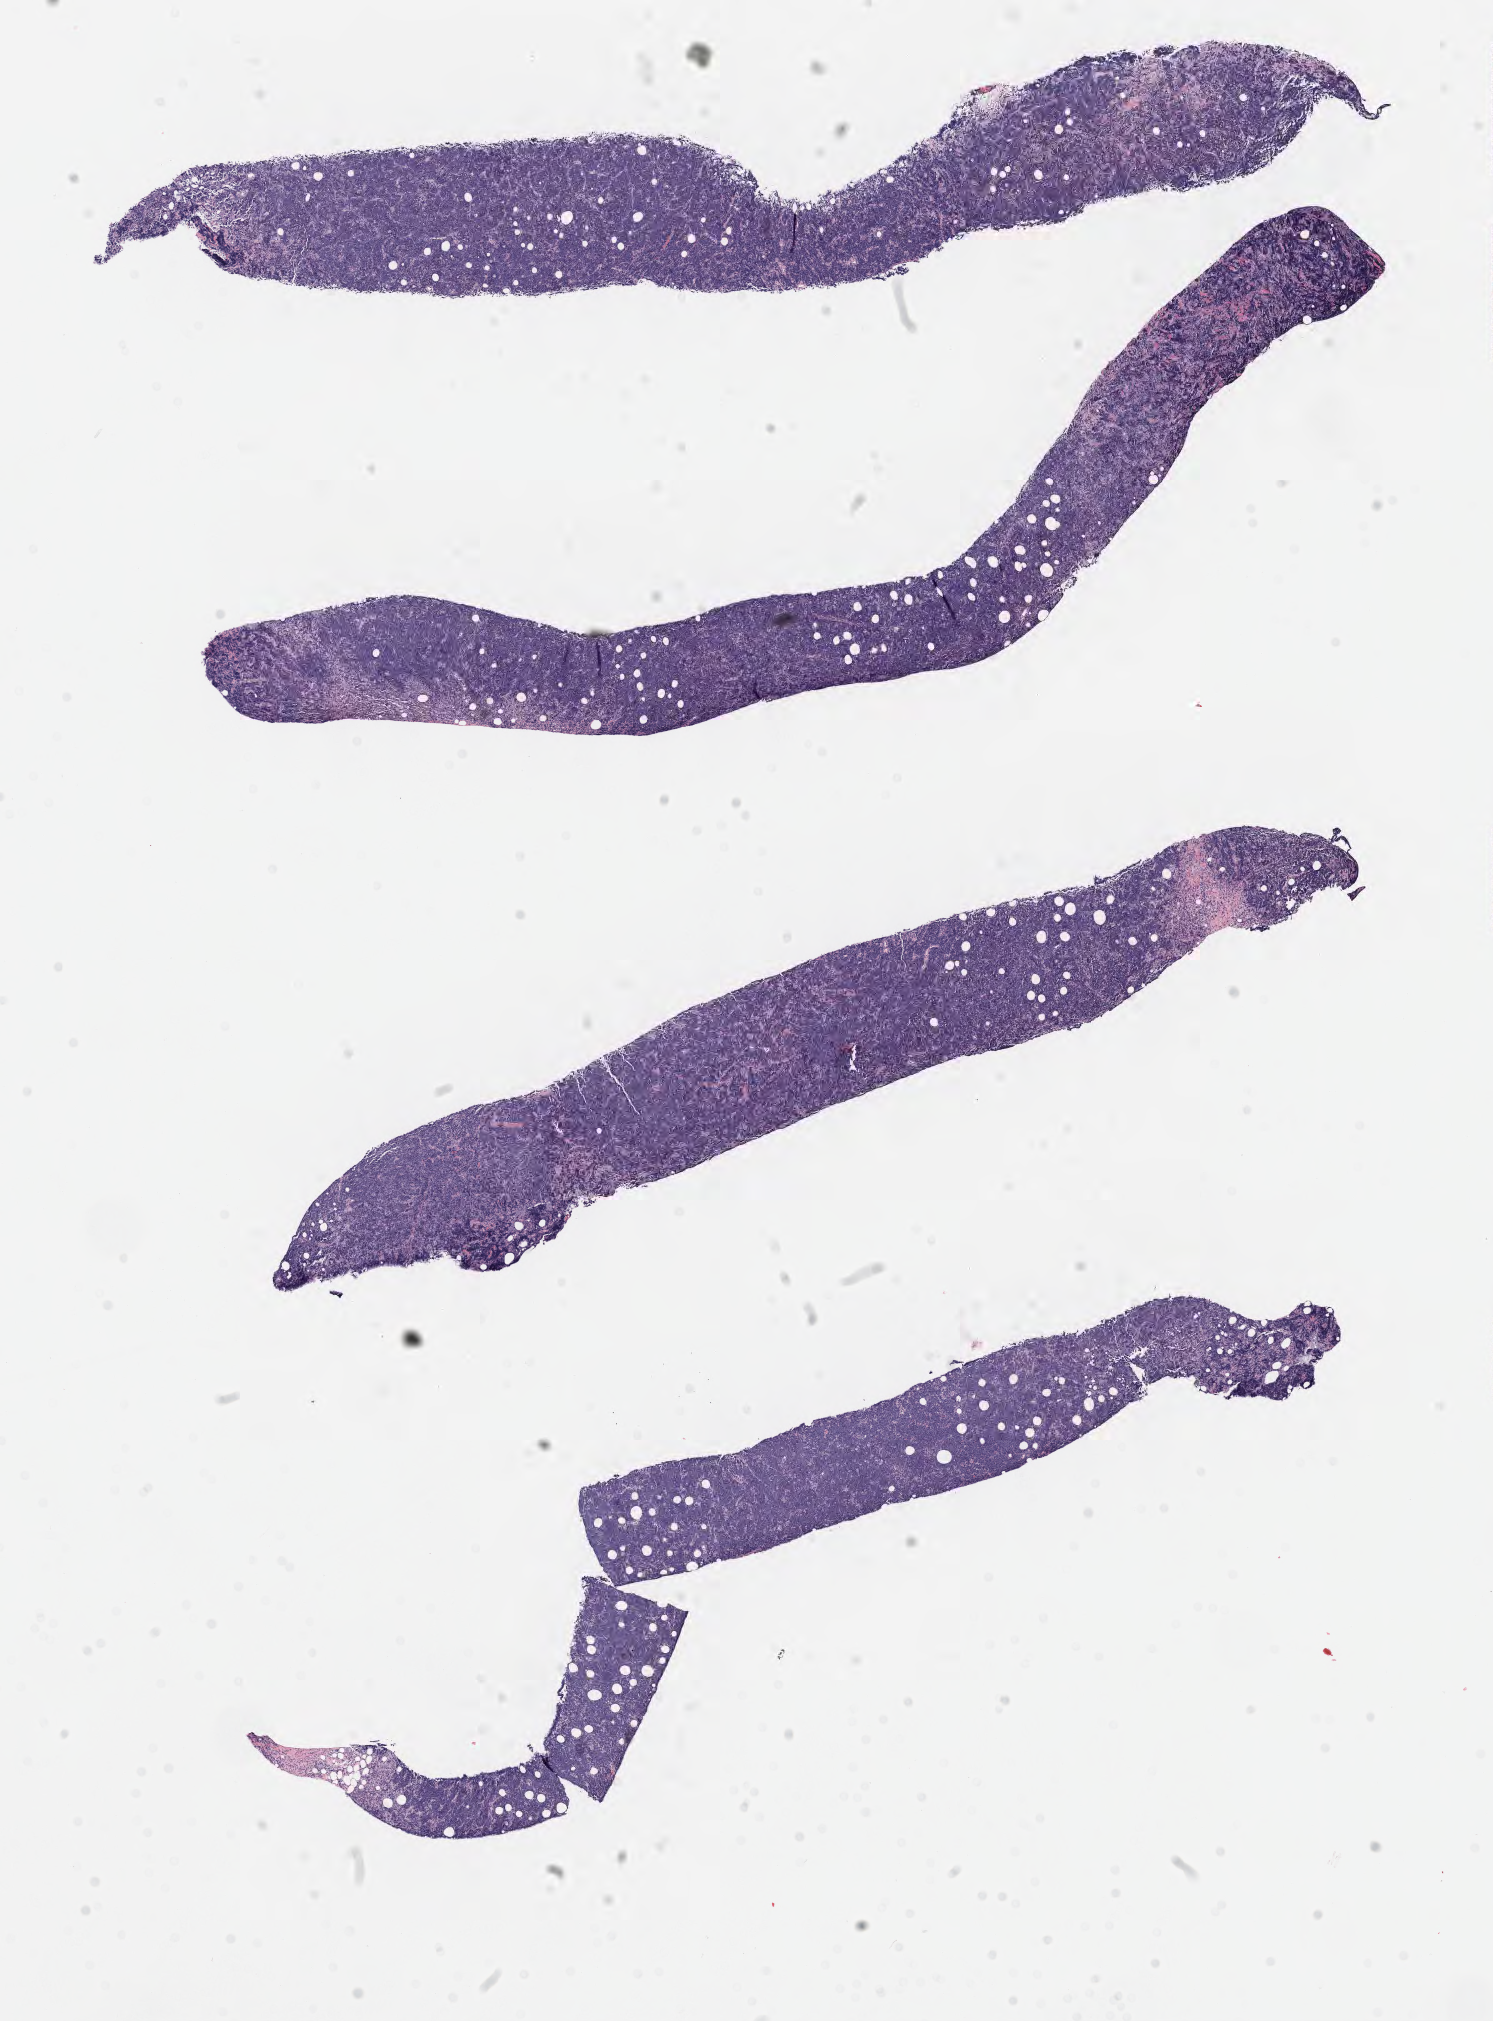
Whole-slide image, hematoxylin and eosin (H&E) stain — whole scanned area (about 12.1 x 16.4 mm) shown as a low-resolution overview; tumor tissue. Patient male; aged 69.
* diagnosis: Diffuse large B-cell lymphoma, NOS